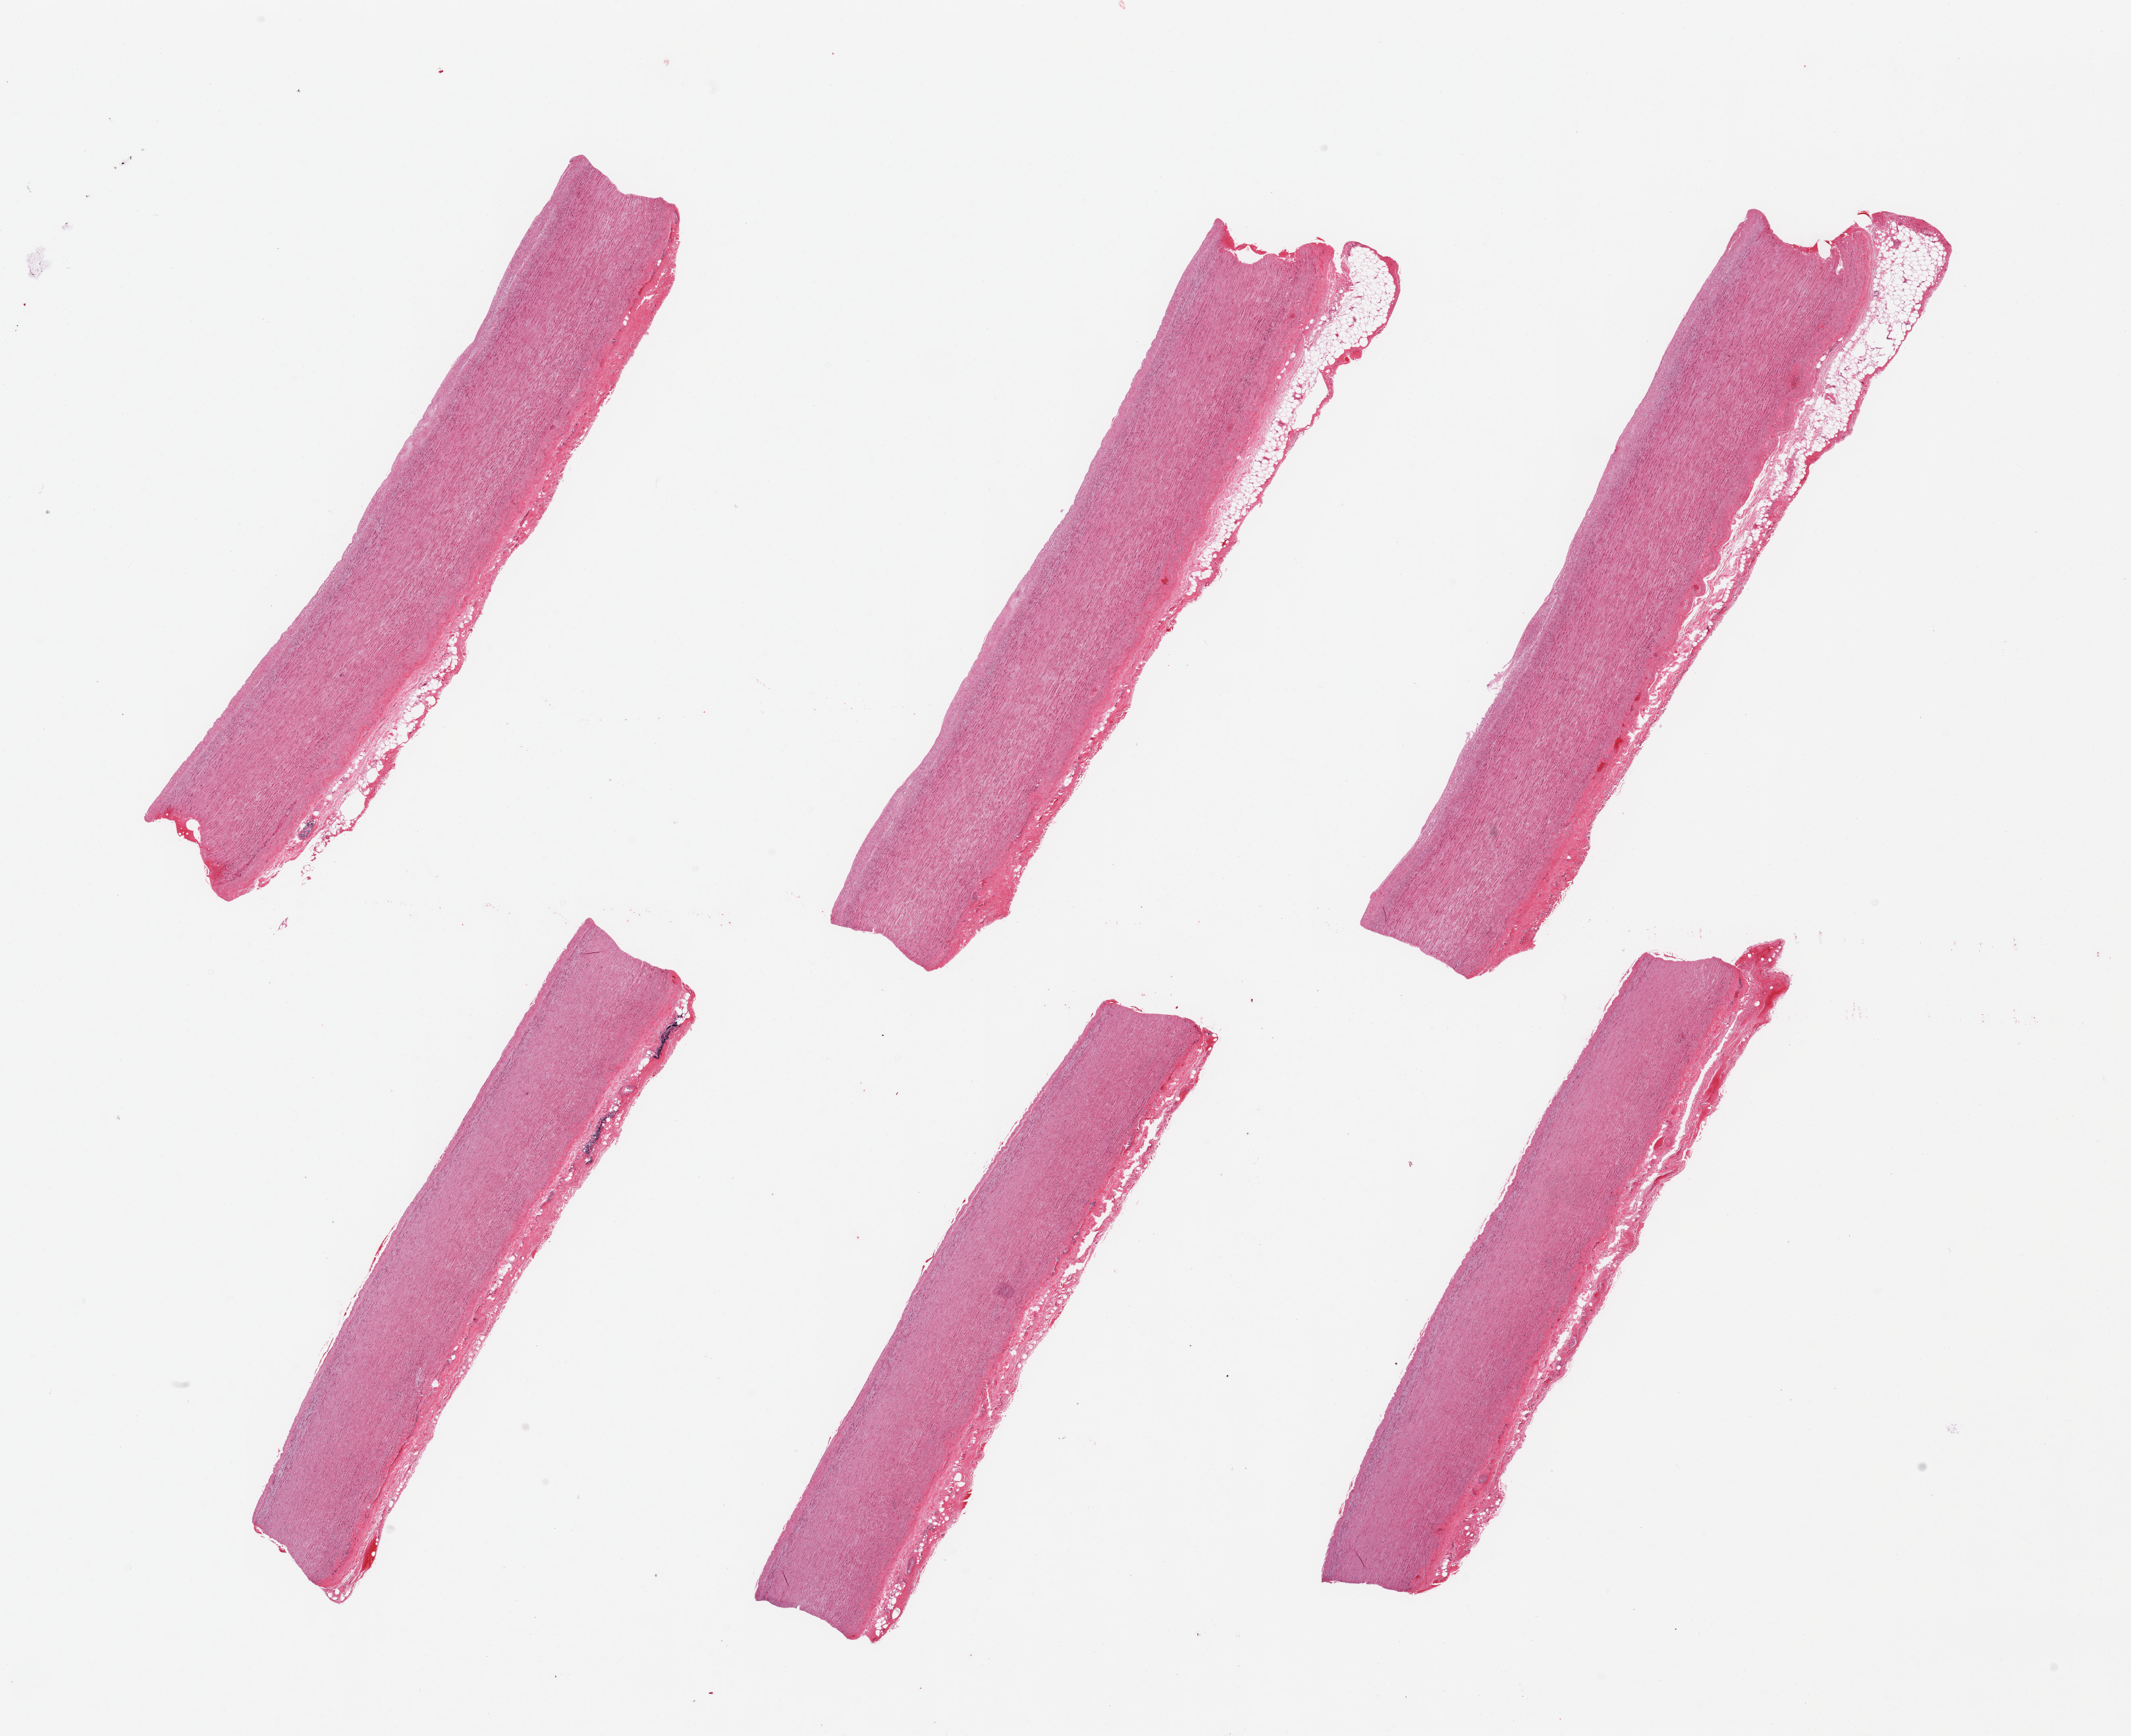
Digitized hematoxylin and eosin (H&E)-stained section — a low-resolution overview of the entire scanned area, about 25.6 x 20.8 mm. PAXgene-fixed paraffin-embedded (PFPE) section. Sampled site (target tissue): aorta. Donor tissue sample. Male donor.
Review note (as recorded): 6 pieces, trace atherosis.